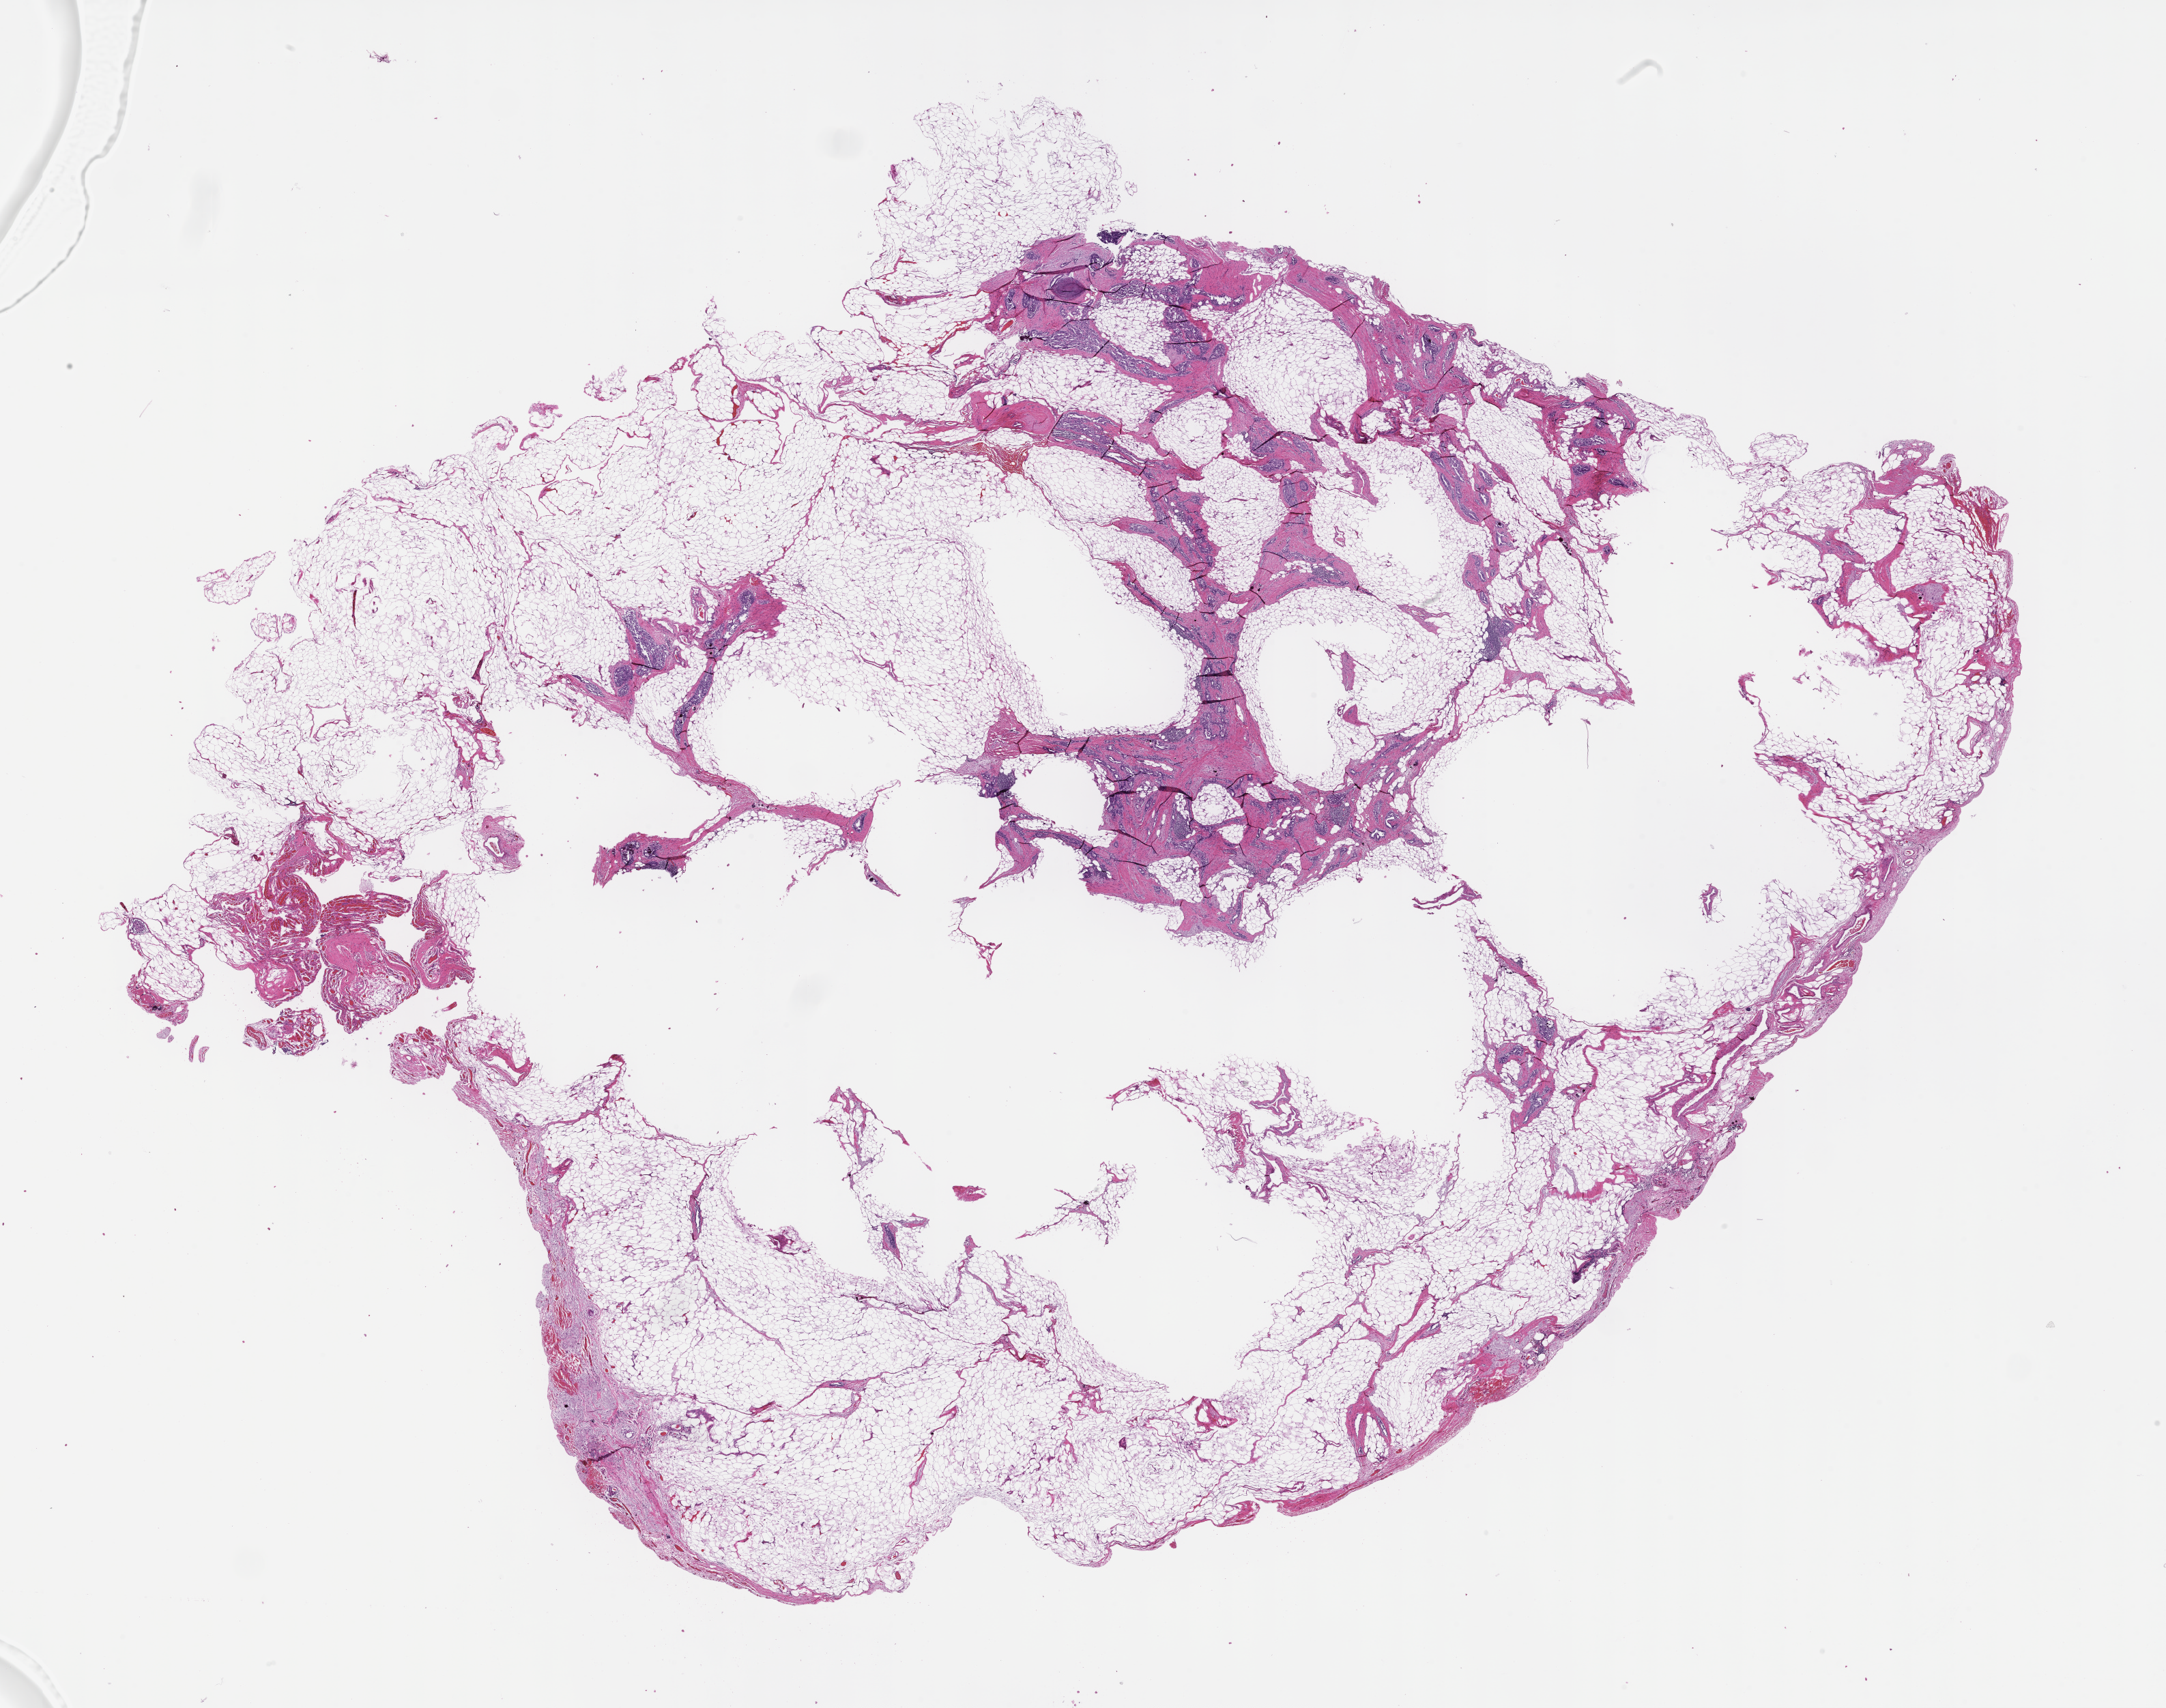
Digitized H&E-stained section, whole scanned area (about 25.6 x 20.2 mm) shown as a low-resolution overview. Formalin-fixed, paraffin-embedded (FFPE) tissue. Collected at baseline (before treatment). Patient sex: female.
- this section: metastatic tumor tissue
- primary diagnosis of the patient: Ovarian Carcinoma